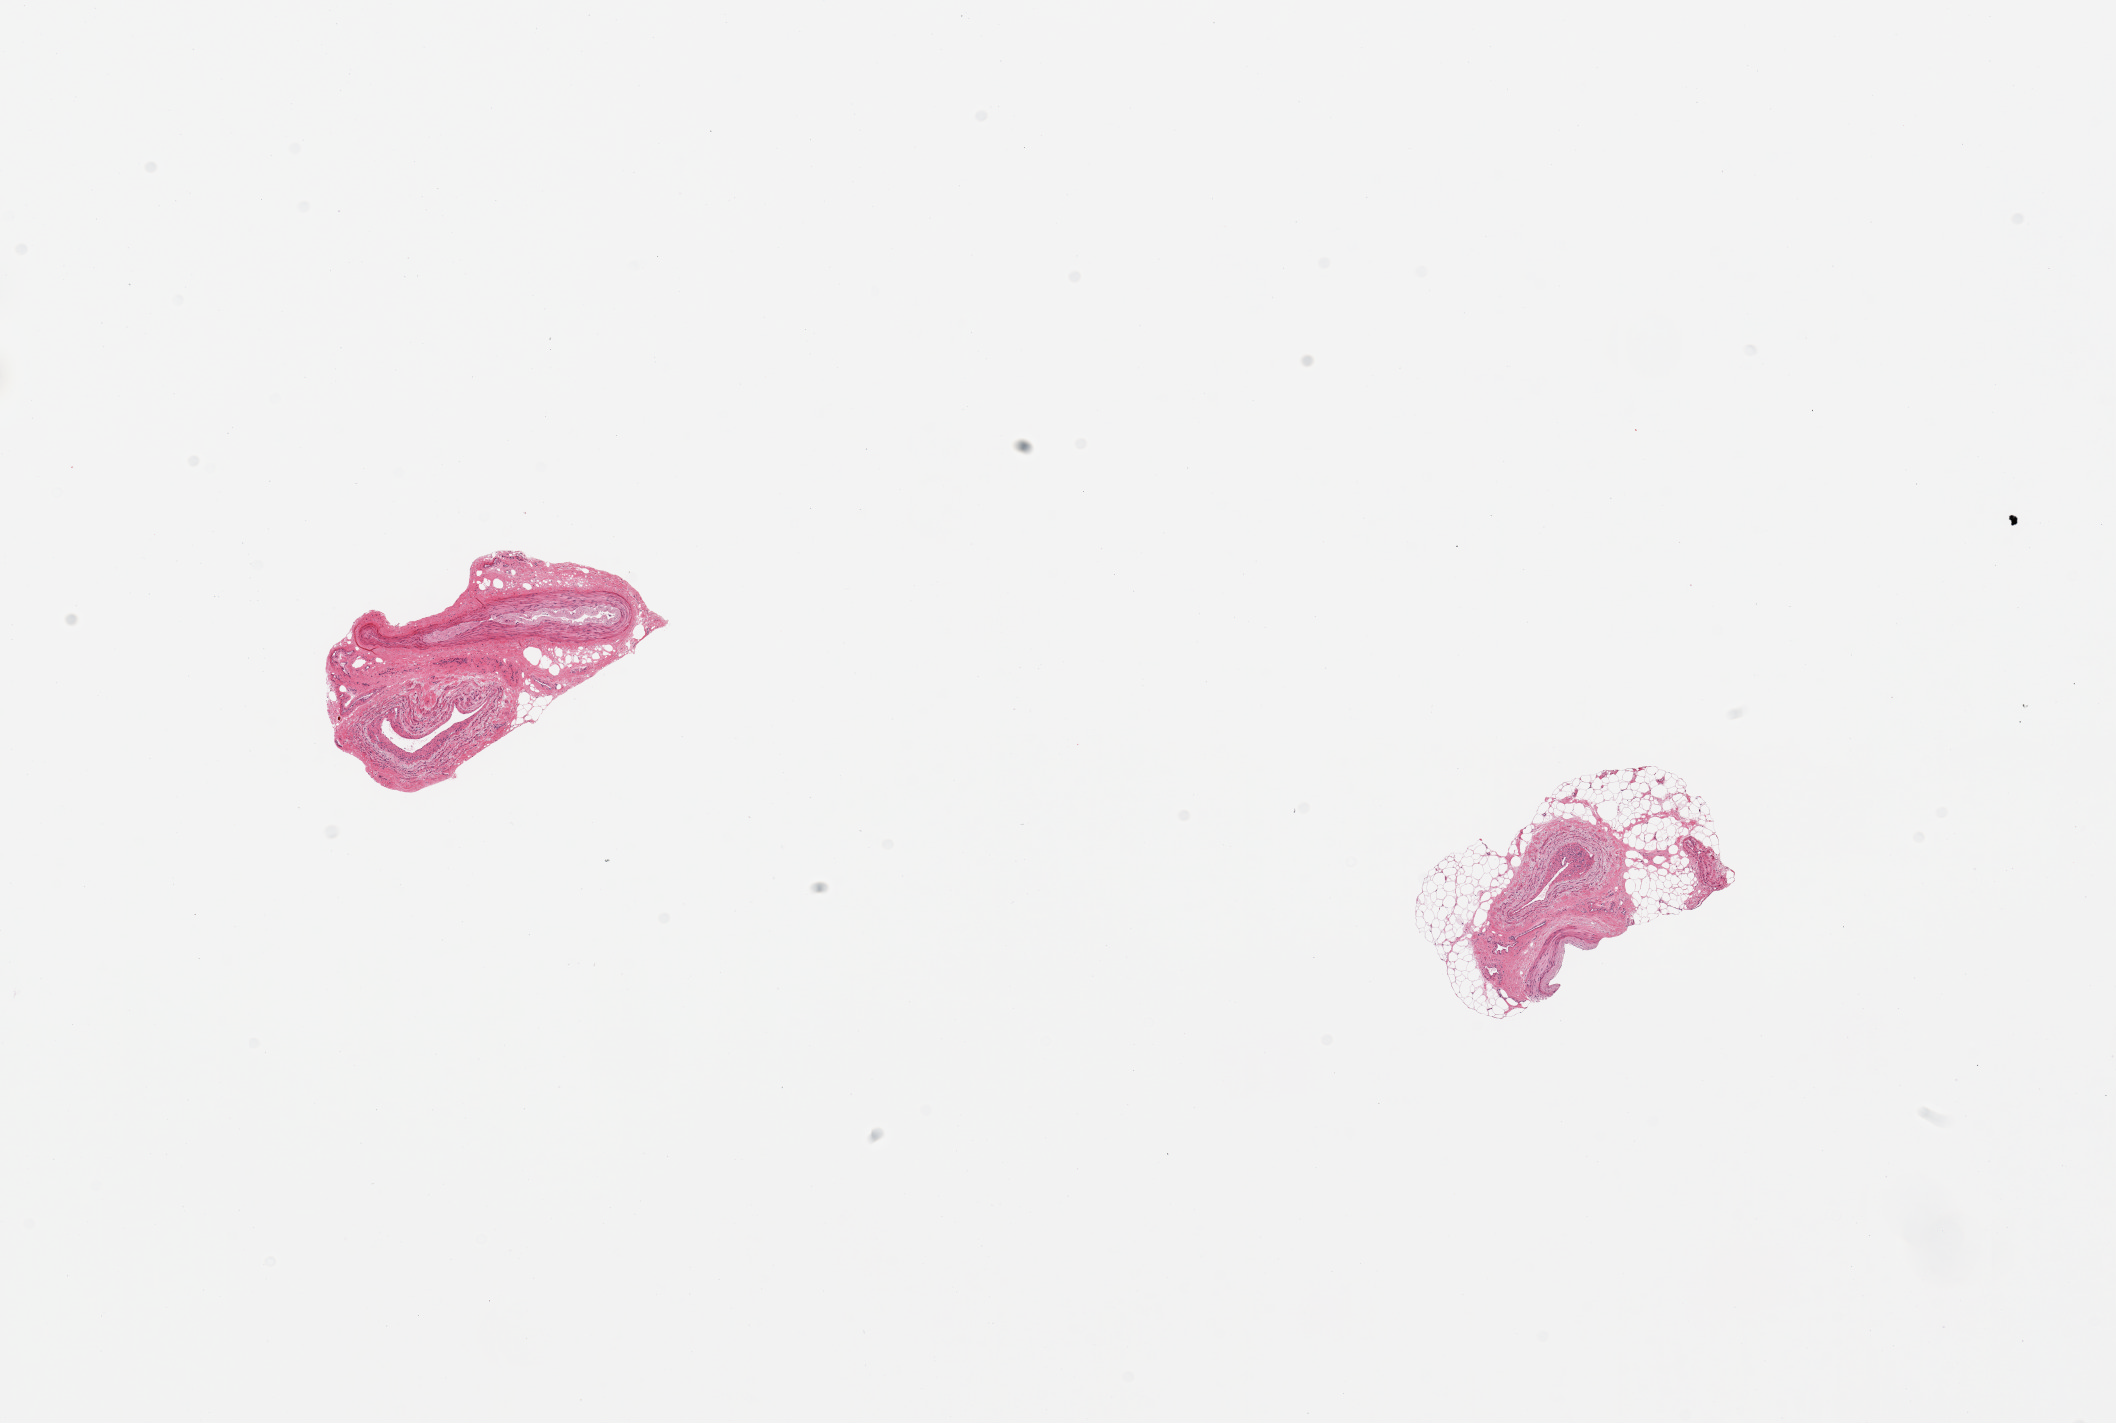
Hematoxylin and eosin (H&E) whole-slide image — low-resolution overview of the scanned area, about 16.7 x 11.3 mm (slide scanned at 20x), PAXgene-fixed, paraffin-embedded tissue, target tissue: tibial artery, donor tissue sample.
Pathologist's review note for this sample: 2 pieces; includes attached fat and vein.